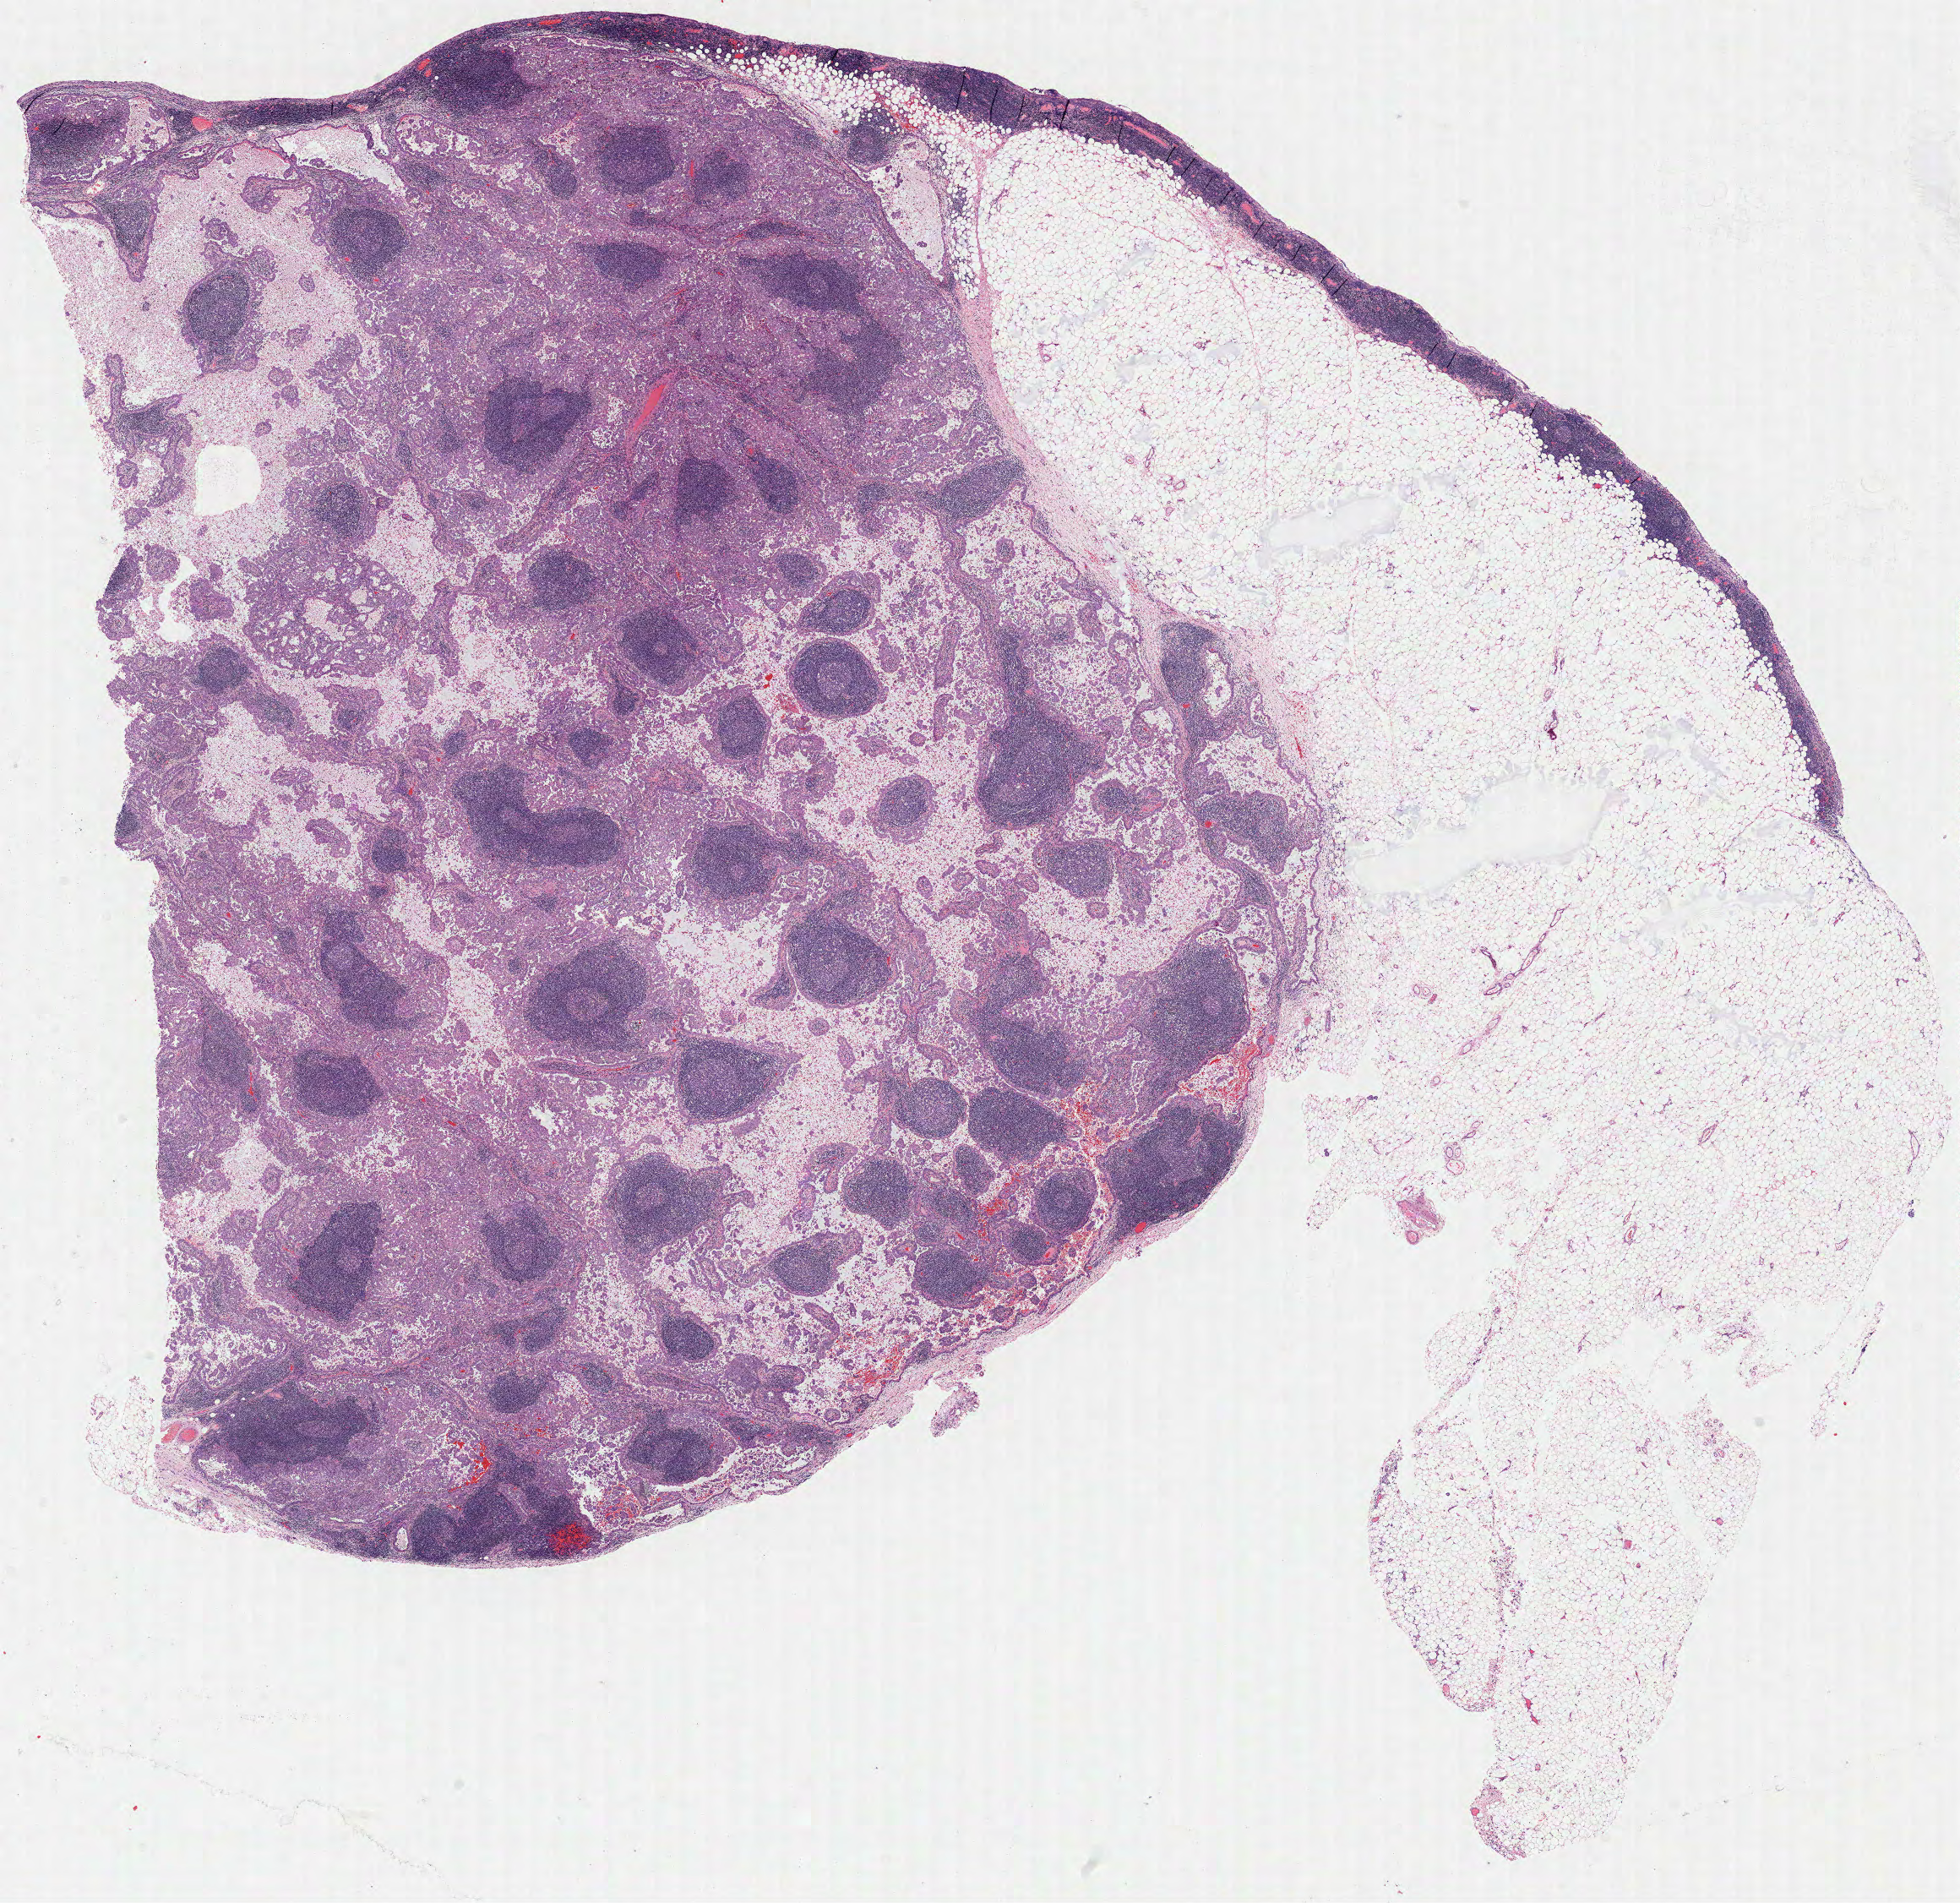
Whole-slide histology image, H&E — whole scanned area (about 18.5 x 18.0 mm) shown as a low-resolution overview; formalin-fixed paraffin-embedded (FFPE) diagnostic section; sample: primary tumour, mesothelium. Female patient; age at initial diagnosis 71 years.
Diagnosis: Epithelioid mesothelioma, malignant.